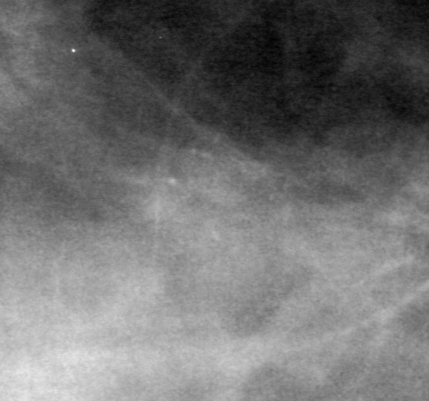
Region of interest cut from a scanned film mammogram (one marked finding); right breast; MLO view; BI-RADS breast density category 3 (scale 1–4).
Finding: calcifications, morphology punctate / amorphous, distribution clustered; BI-RADS assessment category 0 (incomplete: needs additional imaging); pathology (as recorded): benign.